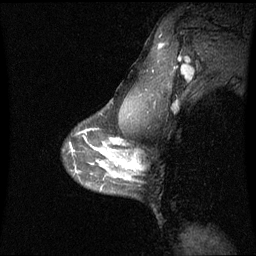
Breast MRI (dynamic contrast-enhanced), one sagittal slice. Position 49 of 60 along the scan axis. Dynamic contrast-enhanced series, image 2 of 3 at this slice position (ordered by acquisition). 1.5 T. TE 4.2 ms, TR 8.9 ms. 256 × 256 image matrix, field of view 230 × 230 mm. Female patient, age 42 years. Case-level facts recorded for this patient, not image findings: setting: breast cancer imaged before/during neoadjuvant chemotherapy; receptor status: triple-negative.
Outlined on this slice (semi-automatically segmented with operator editing):
- analysis volume of interest (the breast-tissue region the enhancement analysis was run in; not a lesion): bounding box <114,150,138,180> (left, top, right, bottom; pixels)
- tumour enhancement mask (voxels above the 70 % enhancement threshold inside the analysis volume of interest): <127,159,138,169>